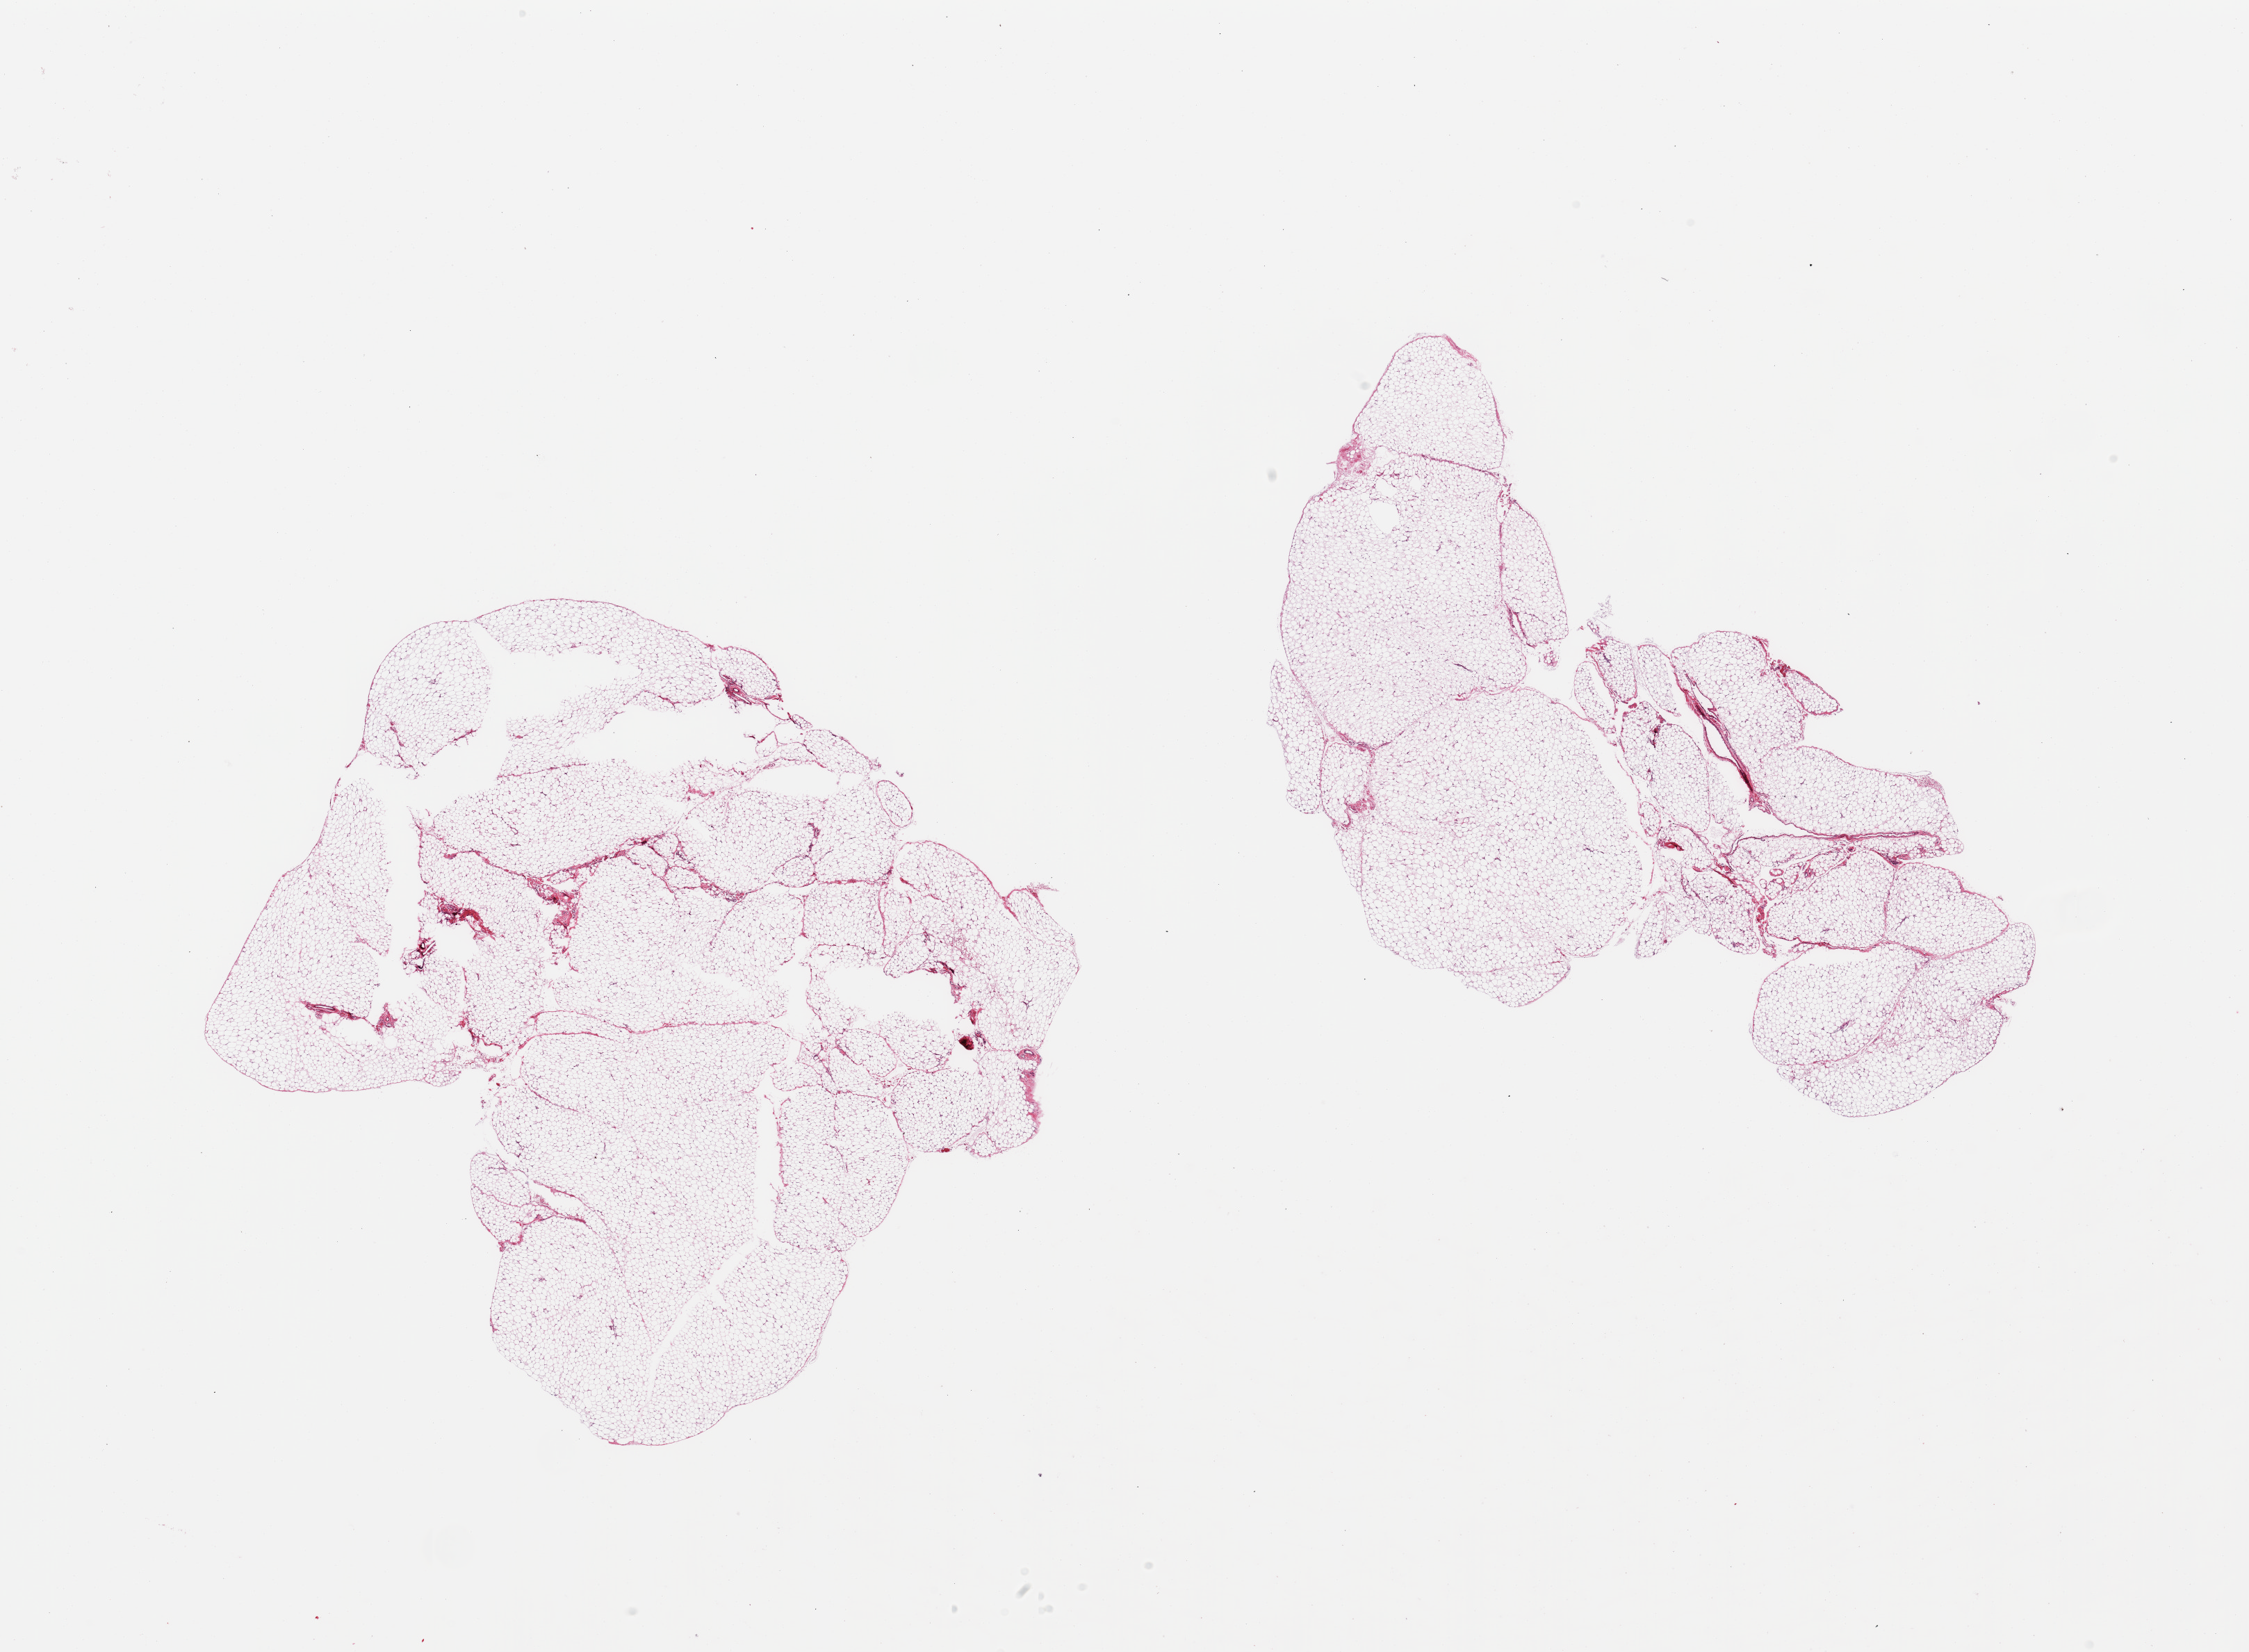
H&E whole-slide image, brightfield, whole scanned area (about 25.6 x 18.8 mm, slide scanned at 20x) shown as a low-resolution overview, PAXgene-fixed paraffin-embedded (PFPE) section, section of omentum (target tissue), donor tissue sample. Donor sex: male.
Reviewer comment on this tissue sample: 2 pieces; <1% fibrous content.